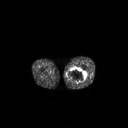
FDG PET of an extremity soft-tissue mass (from a PET/CT study), one axial slice; slice 234 of 267 in the series (ordered by position); 128 × 128 image matrix, field of view 700 × 700 mm. Patient: male, 44 years. Case-level facts recorded for this patient, not image findings: histological type: undifferentiated pleomorphic liposarcoma; grade: high; site of the primary tumour: left thigh.
Annotated regions visible in this slice (expert contour drawn on MRI and transferred to this co-registered scan by the dataset authors):
- gross tumour volume including surrounding oedema: bounding box <67,68,86,83> (left, top, right, bottom; pixels)
- gross tumour volume (mass): <67,68,86,83>